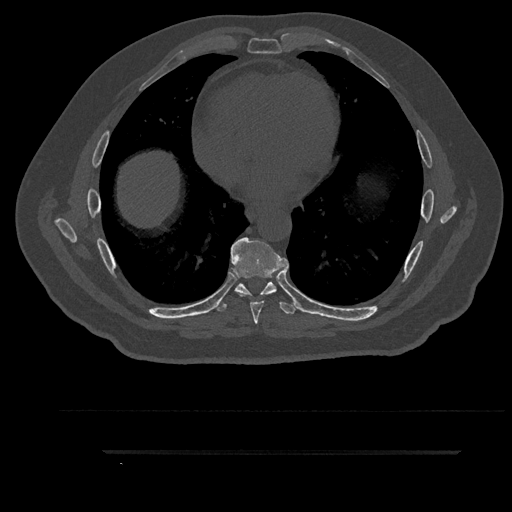
CT including the spine, one axial slice; slice 504 of 797 in the series (ordered by position); reconstruction kernel Br40s/3; bone window (W 1800 / L 400 HU); 0.5 mm slice thickness; 512 × 512 image matrix, field of view 432 × 432 mm. Patient: male, 63 years. Case-level facts recorded for this patient, not image findings: primary cancer: renal.
Structures marked on this image (semi-automatically segmented with operator editing):
- T6 vertebra: box from (x=251, y=293) to (x=269, y=296) px
- T7 vertebra: (x=231, y=237)–(x=289, y=324)
- T8 vertebra: (x=214, y=281)–(x=300, y=314)